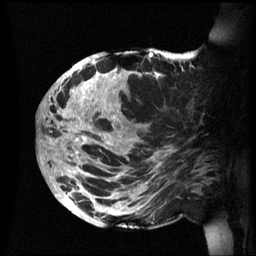
Breast MRI (dynamic contrast-enhanced), one sagittal slice. Position 28 of 60 along the scan axis. Dynamic contrast-enhanced series, image 2 of 3 at this slice position (ordered by acquisition). 1.5 T. TE 4.2 ms, TR 8.4 ms. 2.4 mm slice thickness. 256 × 256 image matrix, field of view 230 × 230 mm. Female patient, age 48 years.
Annotated regions visible in this slice (semi-automatically segmented with operator editing):
- analysis volume of interest (the breast-tissue region the enhancement analysis was run in; not a lesion): bounding box (x1, y1, x2, y2) in pixels: (42, 48, 202, 229)
- tumour enhancement mask (voxels above the 70 % enhancement threshold inside the analysis volume of interest): (42, 52, 169, 226)